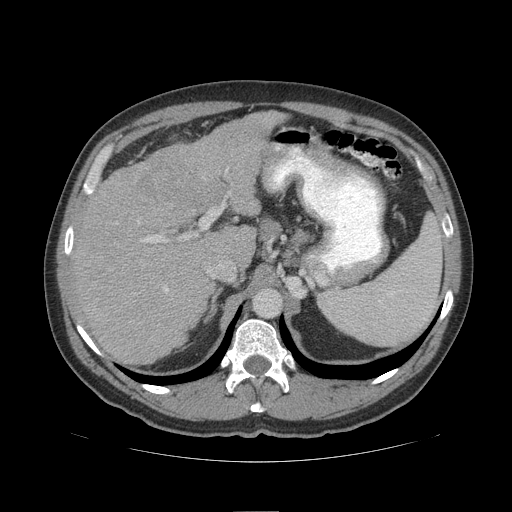
Contrast-enhanced abdominal CT (liver protocol), one axial slice. Position 69 of 109 along the scan axis. Reconstruction kernel STANDARD. 140 kVp. Soft-tissue window (W 400 / L 40 HU). 512 × 512 image matrix, field of view 420 × 420 mm. Case-level facts recorded for this patient, not image findings: diagnosis: hepatocellular carcinoma (patient treated with transarterial chemoembolisation; whether this scan precedes or follows treatment is not stated here); TNM stage (as recorded): Stage-IIIB; Child-Pugh class: A; tumour differentiation: poorly differentiated.
Annotated regions visible in this slice (semi-automatic segmentation, software-assisted and operator-edited):
- liver parenchyma outside the tumour (the mass and vessels are separate outlines, so this box may not span the whole liver): box from (x=72, y=110) to (x=286, y=364) px
- mass: (x=138, y=145)–(x=228, y=211)
- liver vessels: (x=142, y=169)–(x=228, y=292)